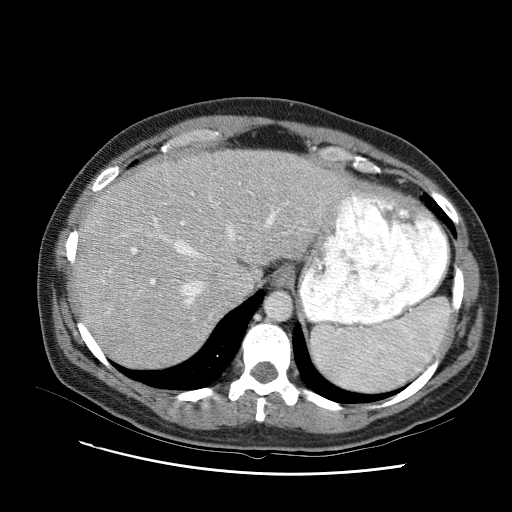
Contrast-enhanced abdominal CT (liver protocol), one axial slice; slice 73 of 95 in the series (ordered by position); 120 kVp; one of 2 acquisitions stored at this slice position; soft-tissue window (W 400 / L 40 HU); 512 × 512 image matrix. From the clinical record (not read from this slice): diagnosis: hepatocellular carcinoma (patient treated with transarterial chemoembolisation; whether this scan precedes or follows treatment is not stated here); TNM stage (as recorded): Stage-I; Child-Pugh class: B.
Outlined on this slice (semi-automatic segmentation, software-assisted and operator-edited):
- liver parenchyma outside the tumour (the mass and vessels are separate outlines, so this box may not span the whole liver): bounding box (x1, y1, x2, y2) in pixels: (74, 148, 344, 352)
- liver vessels: (109, 182, 339, 313)